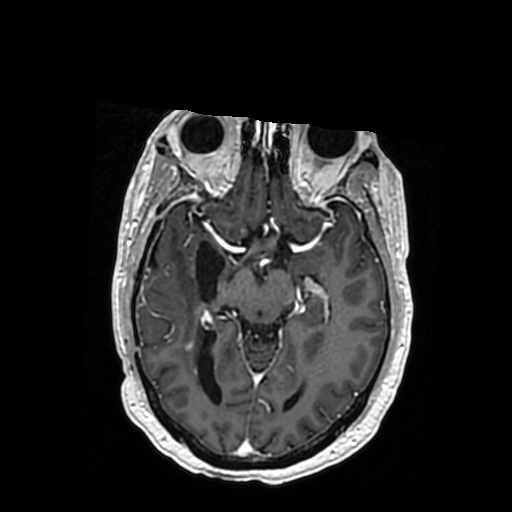
Brain MRI from a brain-tumour surgery series, one axial slice. T1-weighted post-contrast. 0.5 mm slice thickness. 512 × 512 image matrix, field of view 260 × 260 mm. Case-level facts recorded for this patient, not image findings: histopathology: Oligodendroglioma; WHO grade: 3; IDH mutation: yes; tumour location: Right Posterior Temporal Inferior Parietal.
Annotated regions visible in this slice (expert manual segmentation):
- previous resection cavity: bounding box (x1, y1, x2, y2) in pixels: (150, 241, 225, 301)